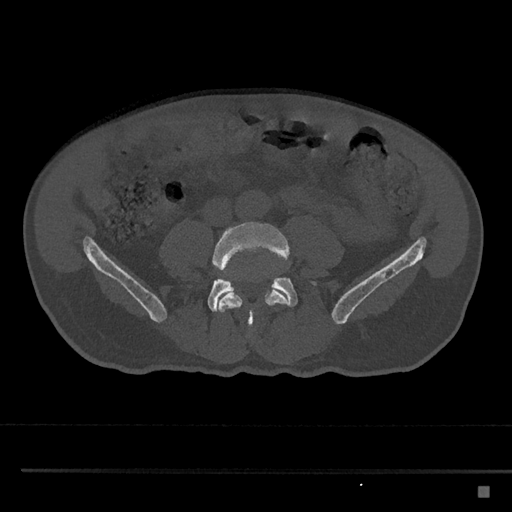
CT including the spine, one axial slice; slice 609 of 797 in the series (ordered by position); reconstruction kernel Br40s/3; 120 kVp; bone window (W 1800 / L 400 HU); 0.5 mm slice thickness; 512 × 512 image matrix, field of view 391 × 391 mm. Patient: male, 59 years. Case-level facts recorded for this patient, not image findings: primary cancer: prostate.
Annotated regions visible in this slice (semi-automatic segmentation, software-assisted and operator-edited):
- L4 vertebra: bounding box [x1, y1, x2, y2] px = [212, 222, 290, 331]
- L5 vertebra: [208, 263, 318, 312]